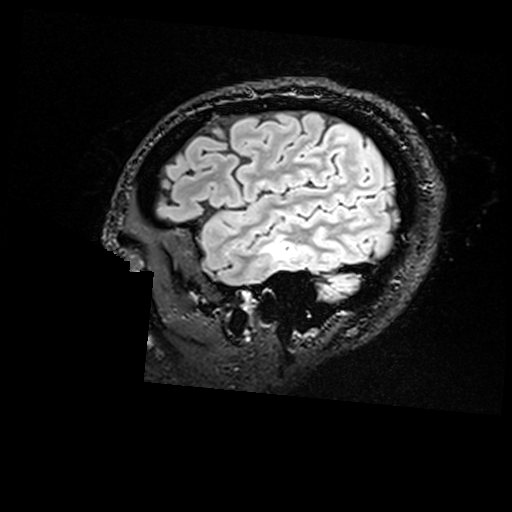
Brain MRI from a brain-tumour surgery series, one sagittal slice. Position 133 of 176 along the scan axis. T2 FLAIR. 512 × 512 image matrix, field of view 250 × 250 mm. Case-level facts recorded for this patient, not image findings: histopathology: Non-tumor destructive chronic inflammatory lesion with abnormal vasculature; tumour location: Right Inferior Temporal.
Outlined on this slice (expert manual segmentation):
- residual tumour: bounding box <280,241,296,259> (left, top, right, bottom; pixels)